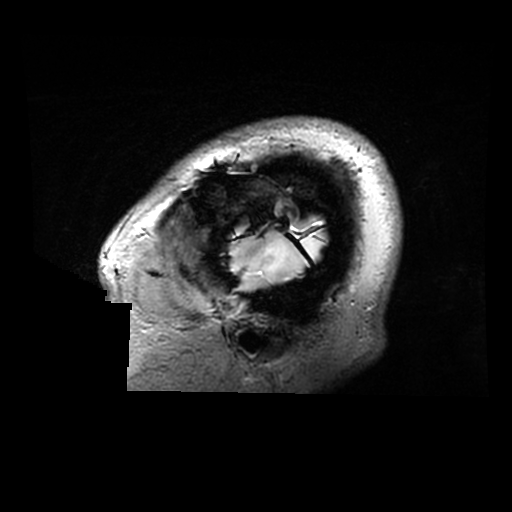
Brain MRI from a brain-tumour surgery series, one sagittal slice; position 260 of 320 along the scan axis; 0.6 mm slice thickness; 512 × 512 image matrix, field of view 240 × 240 mm. Case-level facts recorded for this patient, not image findings: histopathology: Astrocytoma; WHO grade: 2; IDH mutation: yes.
Structures marked on this image (outlined manually by an expert reader):
- tumour: box from (x=229, y=220) to (x=326, y=283) px